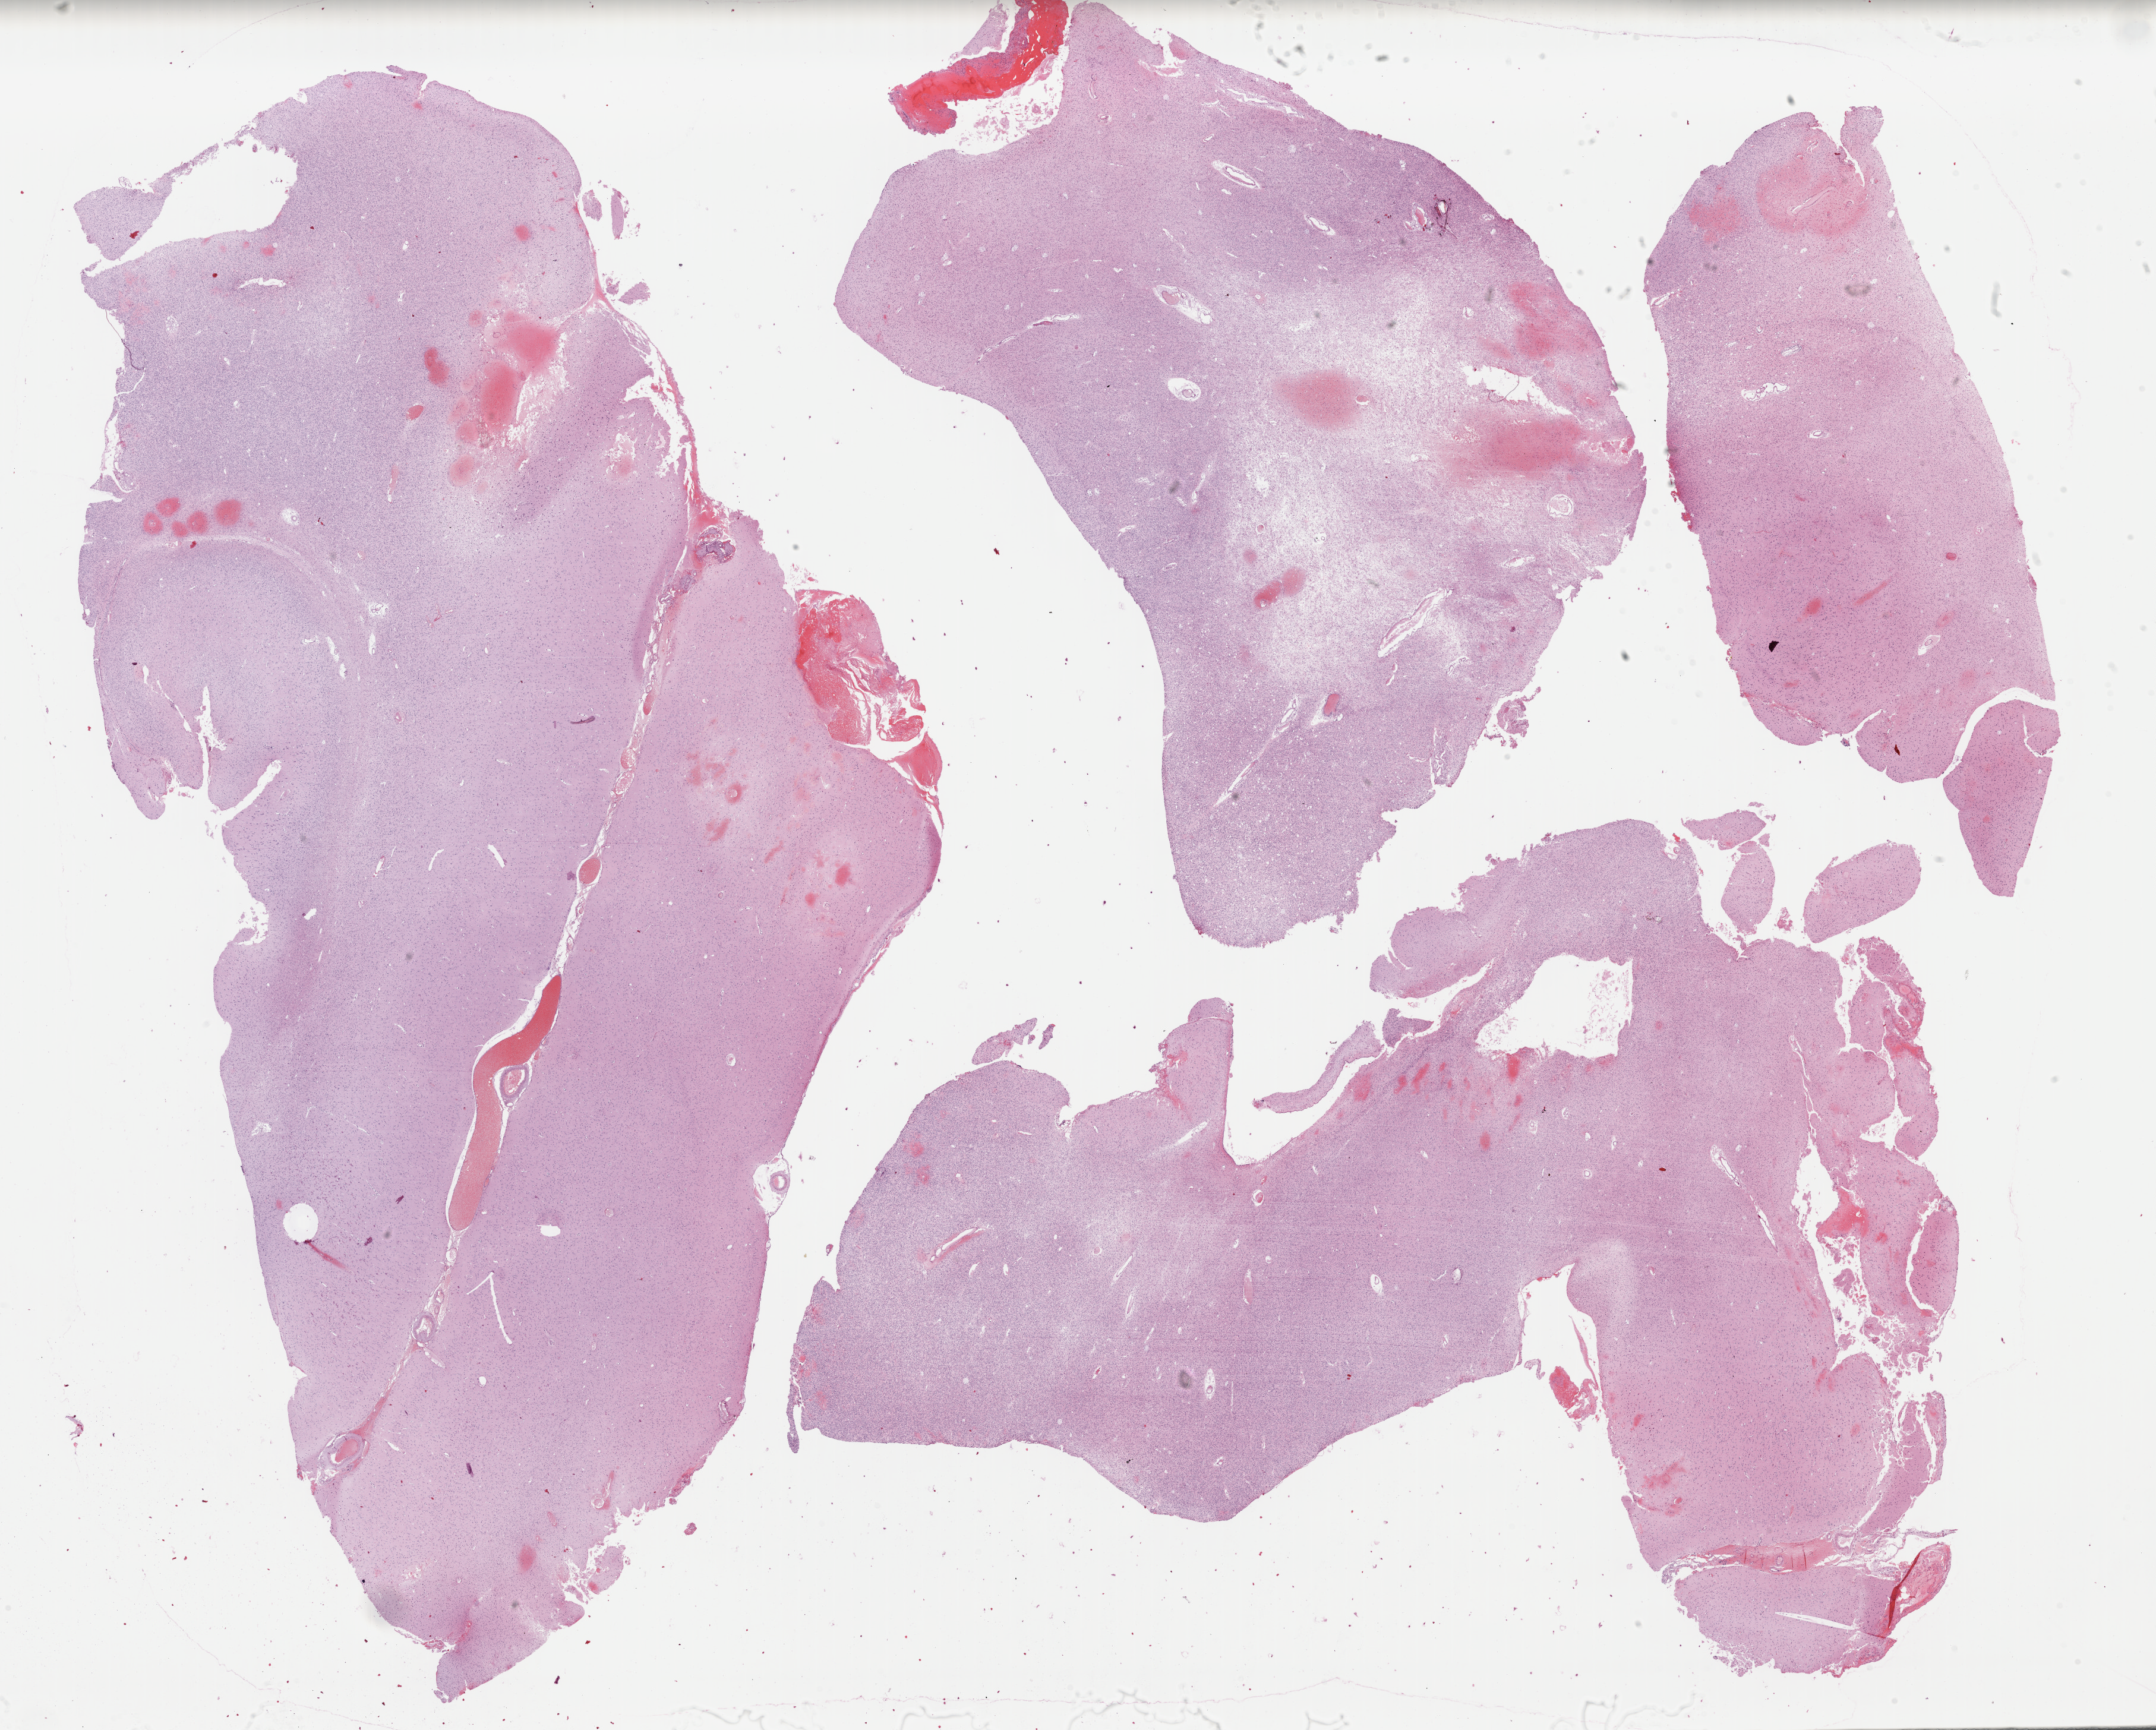
Whole-slide histology image, H&E-stained — whole scanned area (about 28.6 x 23.0 mm, from a 40x scan) shown as a low-resolution overview. Formalin-fixed paraffin-embedded (FFPE) diagnostic section. Primary tumour sample from the brain. Female patient; age at initial diagnosis 43 years. Histologic grade: G2 (moderately differentiated).
Histologic diagnosis: Oligodendroglioma, NOS (cerebrum).